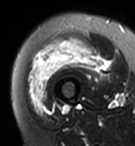
MRI of an extremity soft-tissue mass, one axial slice. Position 26 of 95 along the scan axis. T2-weighted fat-saturated. MR volume resampled by the dataset authors to the PET/CT grid (not the native acquisition matrix). 3.27 mm slice thickness. 135 × 146 image matrix, field of view 132 × 143 mm. Female patient. Case-level facts recorded for this patient, not image findings: histological type: pleiomorphic undifferentiated sarcoma; grade: high; site of the primary tumour: right quadricep.
Annotated regions visible in this slice (expert contour drawn on MRI and transferred to this co-registered scan by the dataset authors):
- gross tumour volume including surrounding oedema: bounding box [x1, y1, x2, y2] px = [28, 38, 104, 112]